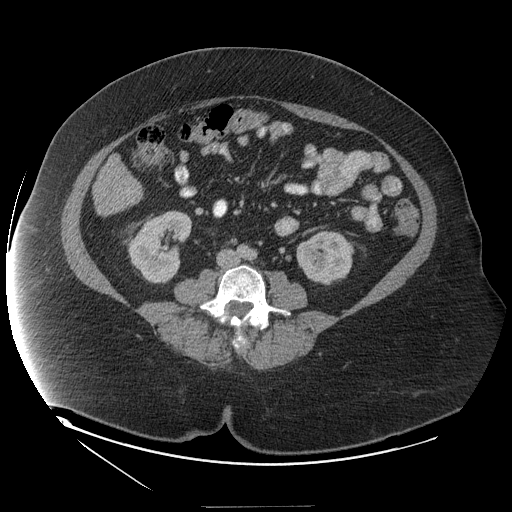
Contrast-enhanced abdominal CT (liver protocol), one axial slice; position 25 of 127 along the scan axis; reconstruction kernel STANDARD; soft-tissue window (W 400 / L 40 HU); 2.5 mm slice thickness; 512 × 512 image matrix, field of view 480 × 480 mm. Case-level facts recorded for this patient, not image findings: diagnosis: hepatocellular carcinoma (patient treated with transarterial chemoembolisation; whether this scan precedes or follows treatment is not stated here); TNM stage (as recorded): Stage-II; Child-Pugh class: A; tumour differentiation: well differentiated; tumour size: 3 cm.
Annotated regions visible in this slice (semi-automatically segmented with operator editing):
- liver parenchyma outside the tumour (the mass and vessels are separate outlines, so this box may not span the whole liver): bounding box <92,168,132,215> (left, top, right, bottom; pixels)